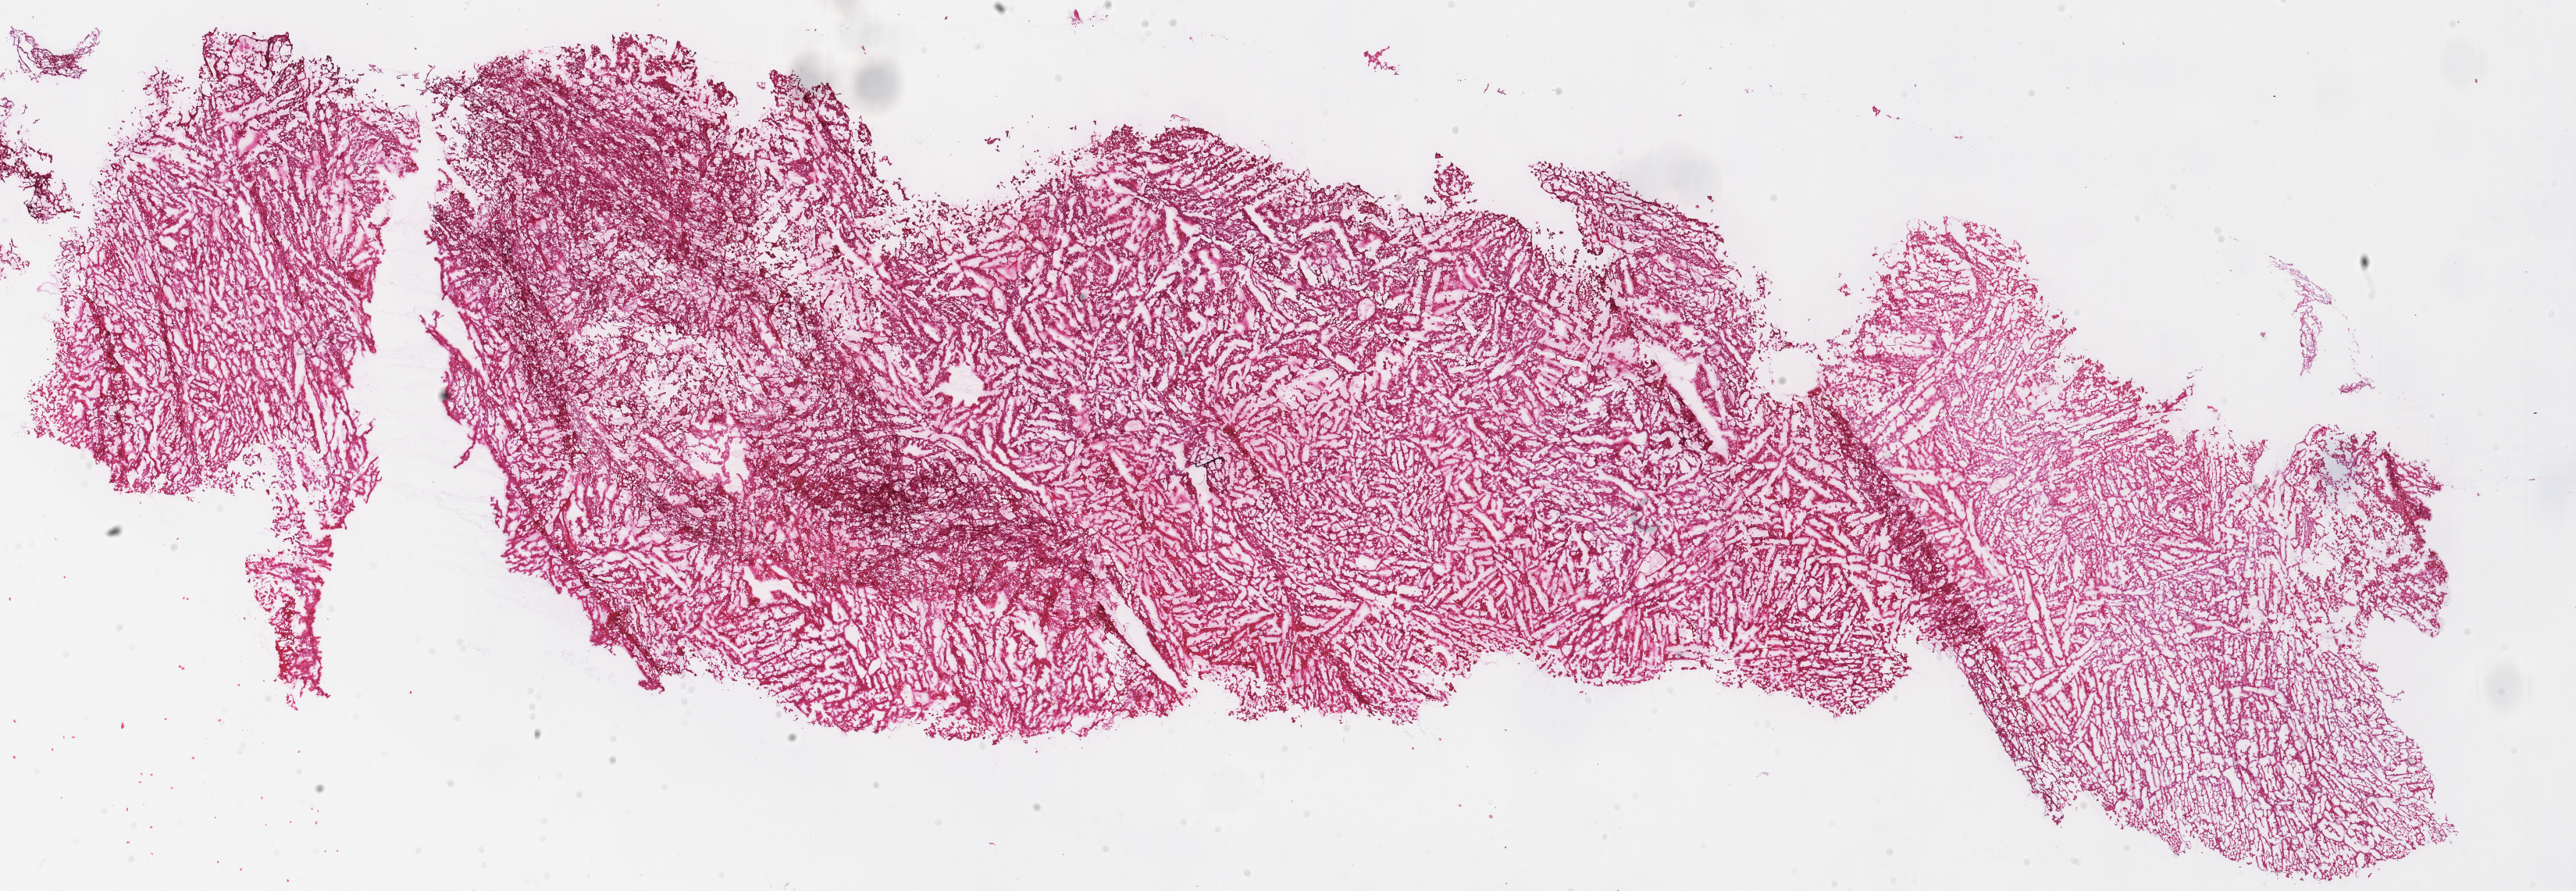
Whole-slide histology image, H&E-stained, a low-resolution overview of the entire scanned area, about 25.9 x 9.0 mm (from a 40x scan); frozen section from the top of the tissue portion; sample: primary tumour, kidney. Male, age 69 years at initial diagnosis. Composition of this section per pathologist review: tumour cells 90%, tumour nuclei 90%, normal cells 0%, stromal cells 10%, necrosis 0%.
TNM: T2b N0 M0. Diagnosis: Renal cell carcinoma, chromophobe type. Lymph nodes positive (case pathology): 0 of 1 examined. AJCC pathologic stage: II (7th edition). Laterality: left.